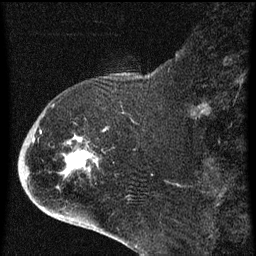
Breast MRI (dynamic contrast-enhanced), one sagittal slice; slice 20 of 60 in the series (ordered by position); dynamic contrast-enhanced series, image 2 of 4 at this slice position (ordered by acquisition); 1.5 T; TE 4.2 ms, TR 8 ms; 2 mm slice thickness; 256 × 256 image matrix, field of view 180 × 180 mm. Female patient, age 71 years.
Annotated regions visible in this slice (semi-automatic segmentation, software-assisted and operator-edited):
- analysis volume of interest (the breast-tissue region the enhancement analysis was run in; not a lesion): bounding box <32,86,131,205> (left, top, right, bottom; pixels)
- tumour enhancement mask (voxels above the 70 % enhancement threshold inside the analysis volume of interest): <40,130,106,171>